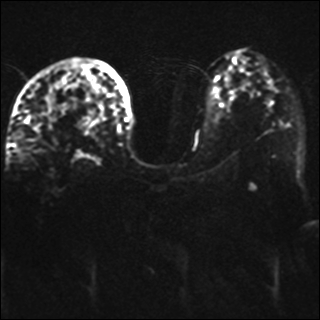
Breast MRI, one axial slice; position 20 of 42 along the scan axis; diffusion-weighted series; image 2 of 4 stored at this slice position (different b-values; order by instance number); 1.5 T; 4 mm slice thickness; 320 × 320 image matrix, field of view 330 × 330 mm. Female patient.
Structures marked on this image (outlined manually by an expert reader):
- tumour on diffusion-weighted imaging: bounding box [x1, y1, x2, y2] px = [45, 98, 56, 119]